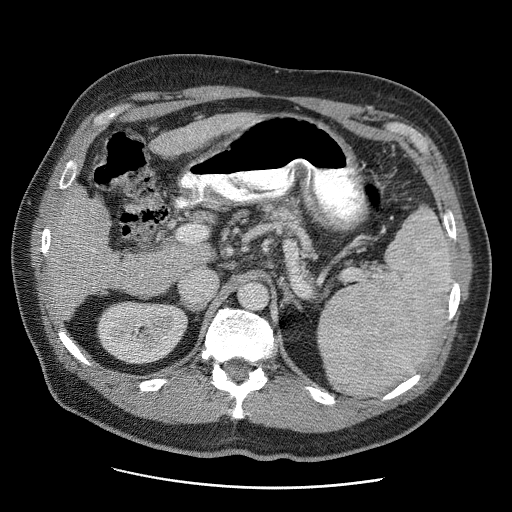
Contrast-enhanced abdominal CT (liver protocol), one axial slice; slice 22 of 81 in the series (ordered by position); reconstruction kernel STANDARD; 120 kVp; soft-tissue window (W 400 / L 40 HU); 2.5 mm slice thickness; 512 × 512 image matrix, field of view 380 × 380 mm. Case-level facts recorded for this patient, not image findings: diagnosis: hepatocellular carcinoma (patient treated with transarterial chemoembolisation; whether this scan precedes or follows treatment is not stated here); TNM stage (as recorded): Stage-IIIA; Child-Pugh class: A; tumour differentiation: moderately differentiated; tumour nodularity: multinodular.
Outlined on this slice (semi-automatically segmented with operator editing):
- abdominal aorta: bounding box [x1, y1, x2, y2] px = [239, 283, 268, 310]
- liver parenchyma outside the tumour (the mass and vessels are separate outlines, so this box may not span the whole liver): [48, 112, 261, 314]